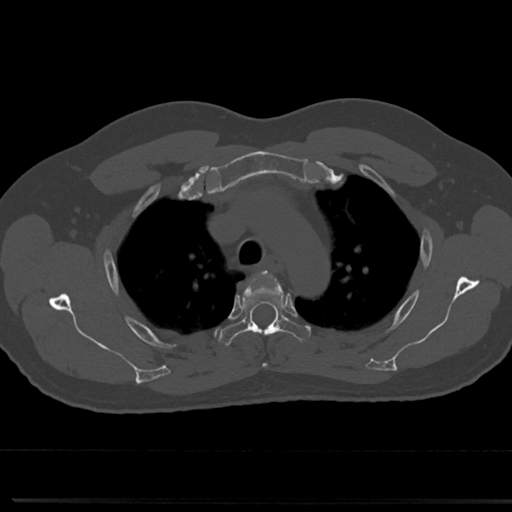
CT including the spine, one axial slice. Position 558 of 817 along the scan axis. Reconstruction kernel Br40s/3. Bone window (W 1800 / L 400 HU). 0.5 mm slice thickness. 512 × 512 image matrix. Patient: male, 61 years. Case-level facts recorded for this patient, not image findings: primary cancer: prostate.
Annotated regions visible in this slice (semi-automatically segmented with operator editing):
- T3 vertebra: bounding box [x1, y1, x2, y2] px = [263, 271, 267, 367]
- T4 vertebra: [219, 271, 310, 345]